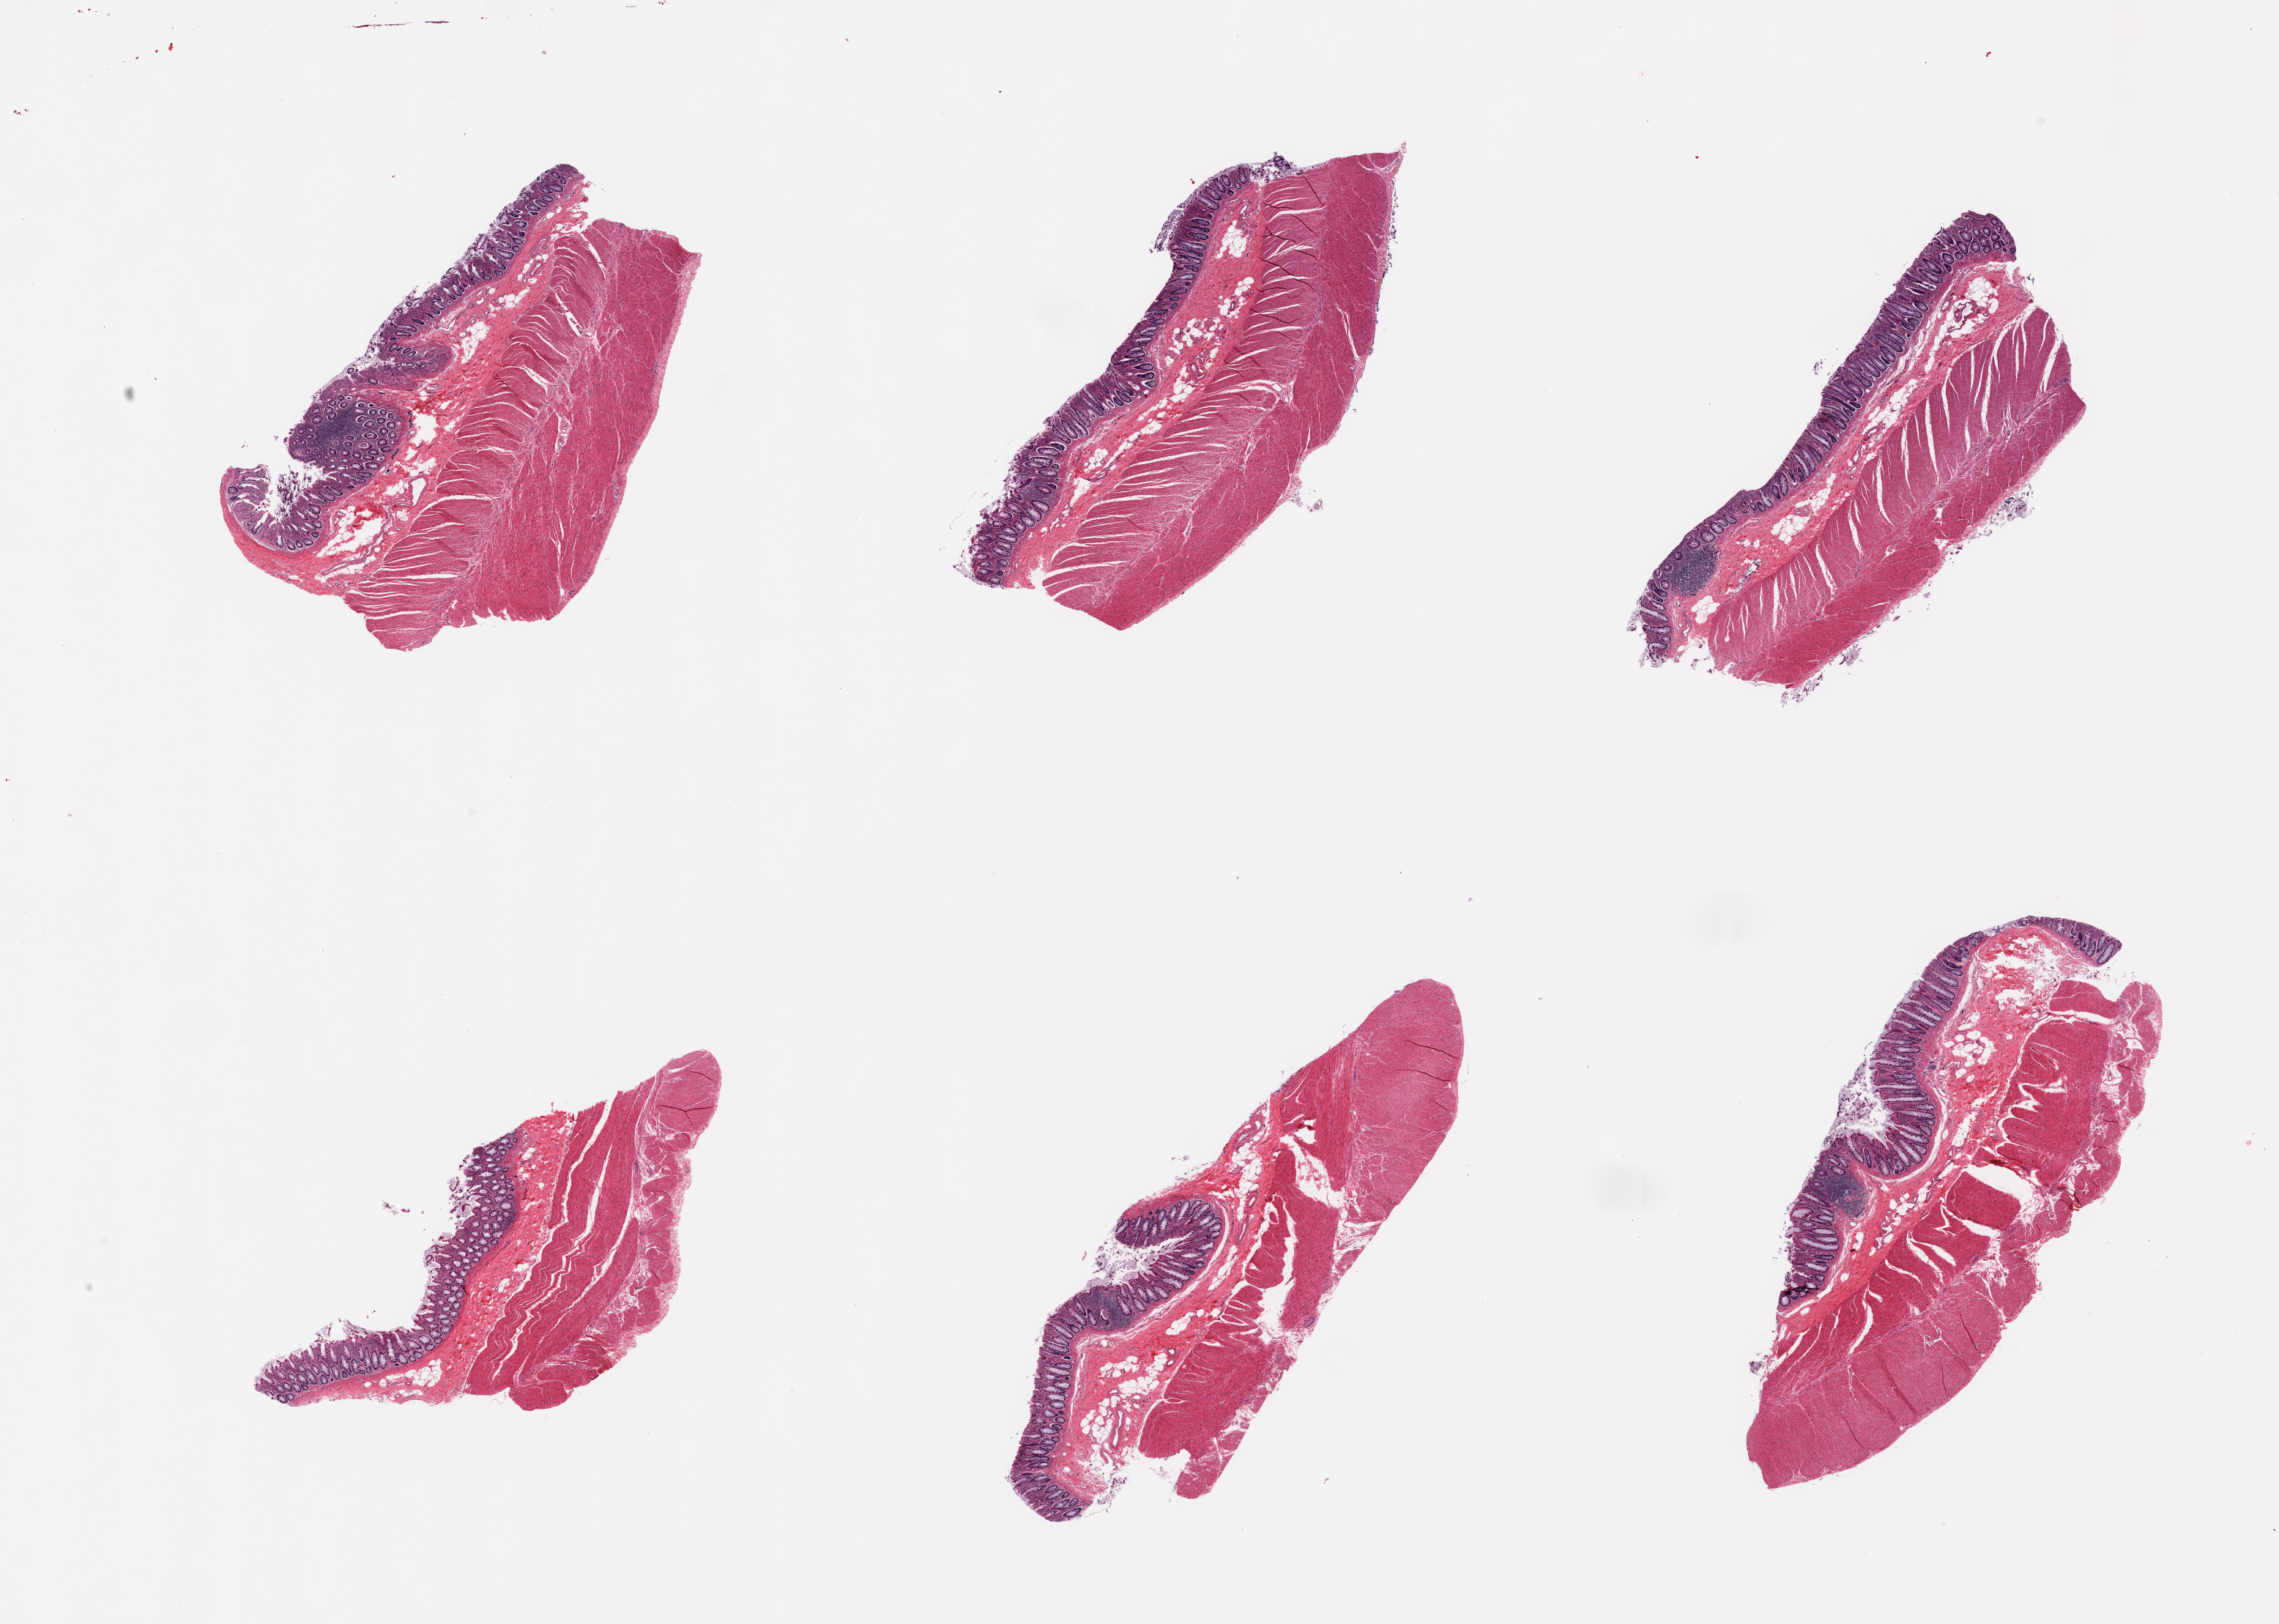
Digitized haematoxylin and eosin-stained section — low-resolution overview of the scanned area, about 24.6 x 17.5 mm; PAXgene-fixed, paraffin-embedded tissue; section of sigmoid colon (target tissue); donor tissue sample.
- reviewer comment on this tissue sample: 6 pieces, target muscularis, ~15-20% 'contaminant' mucosa